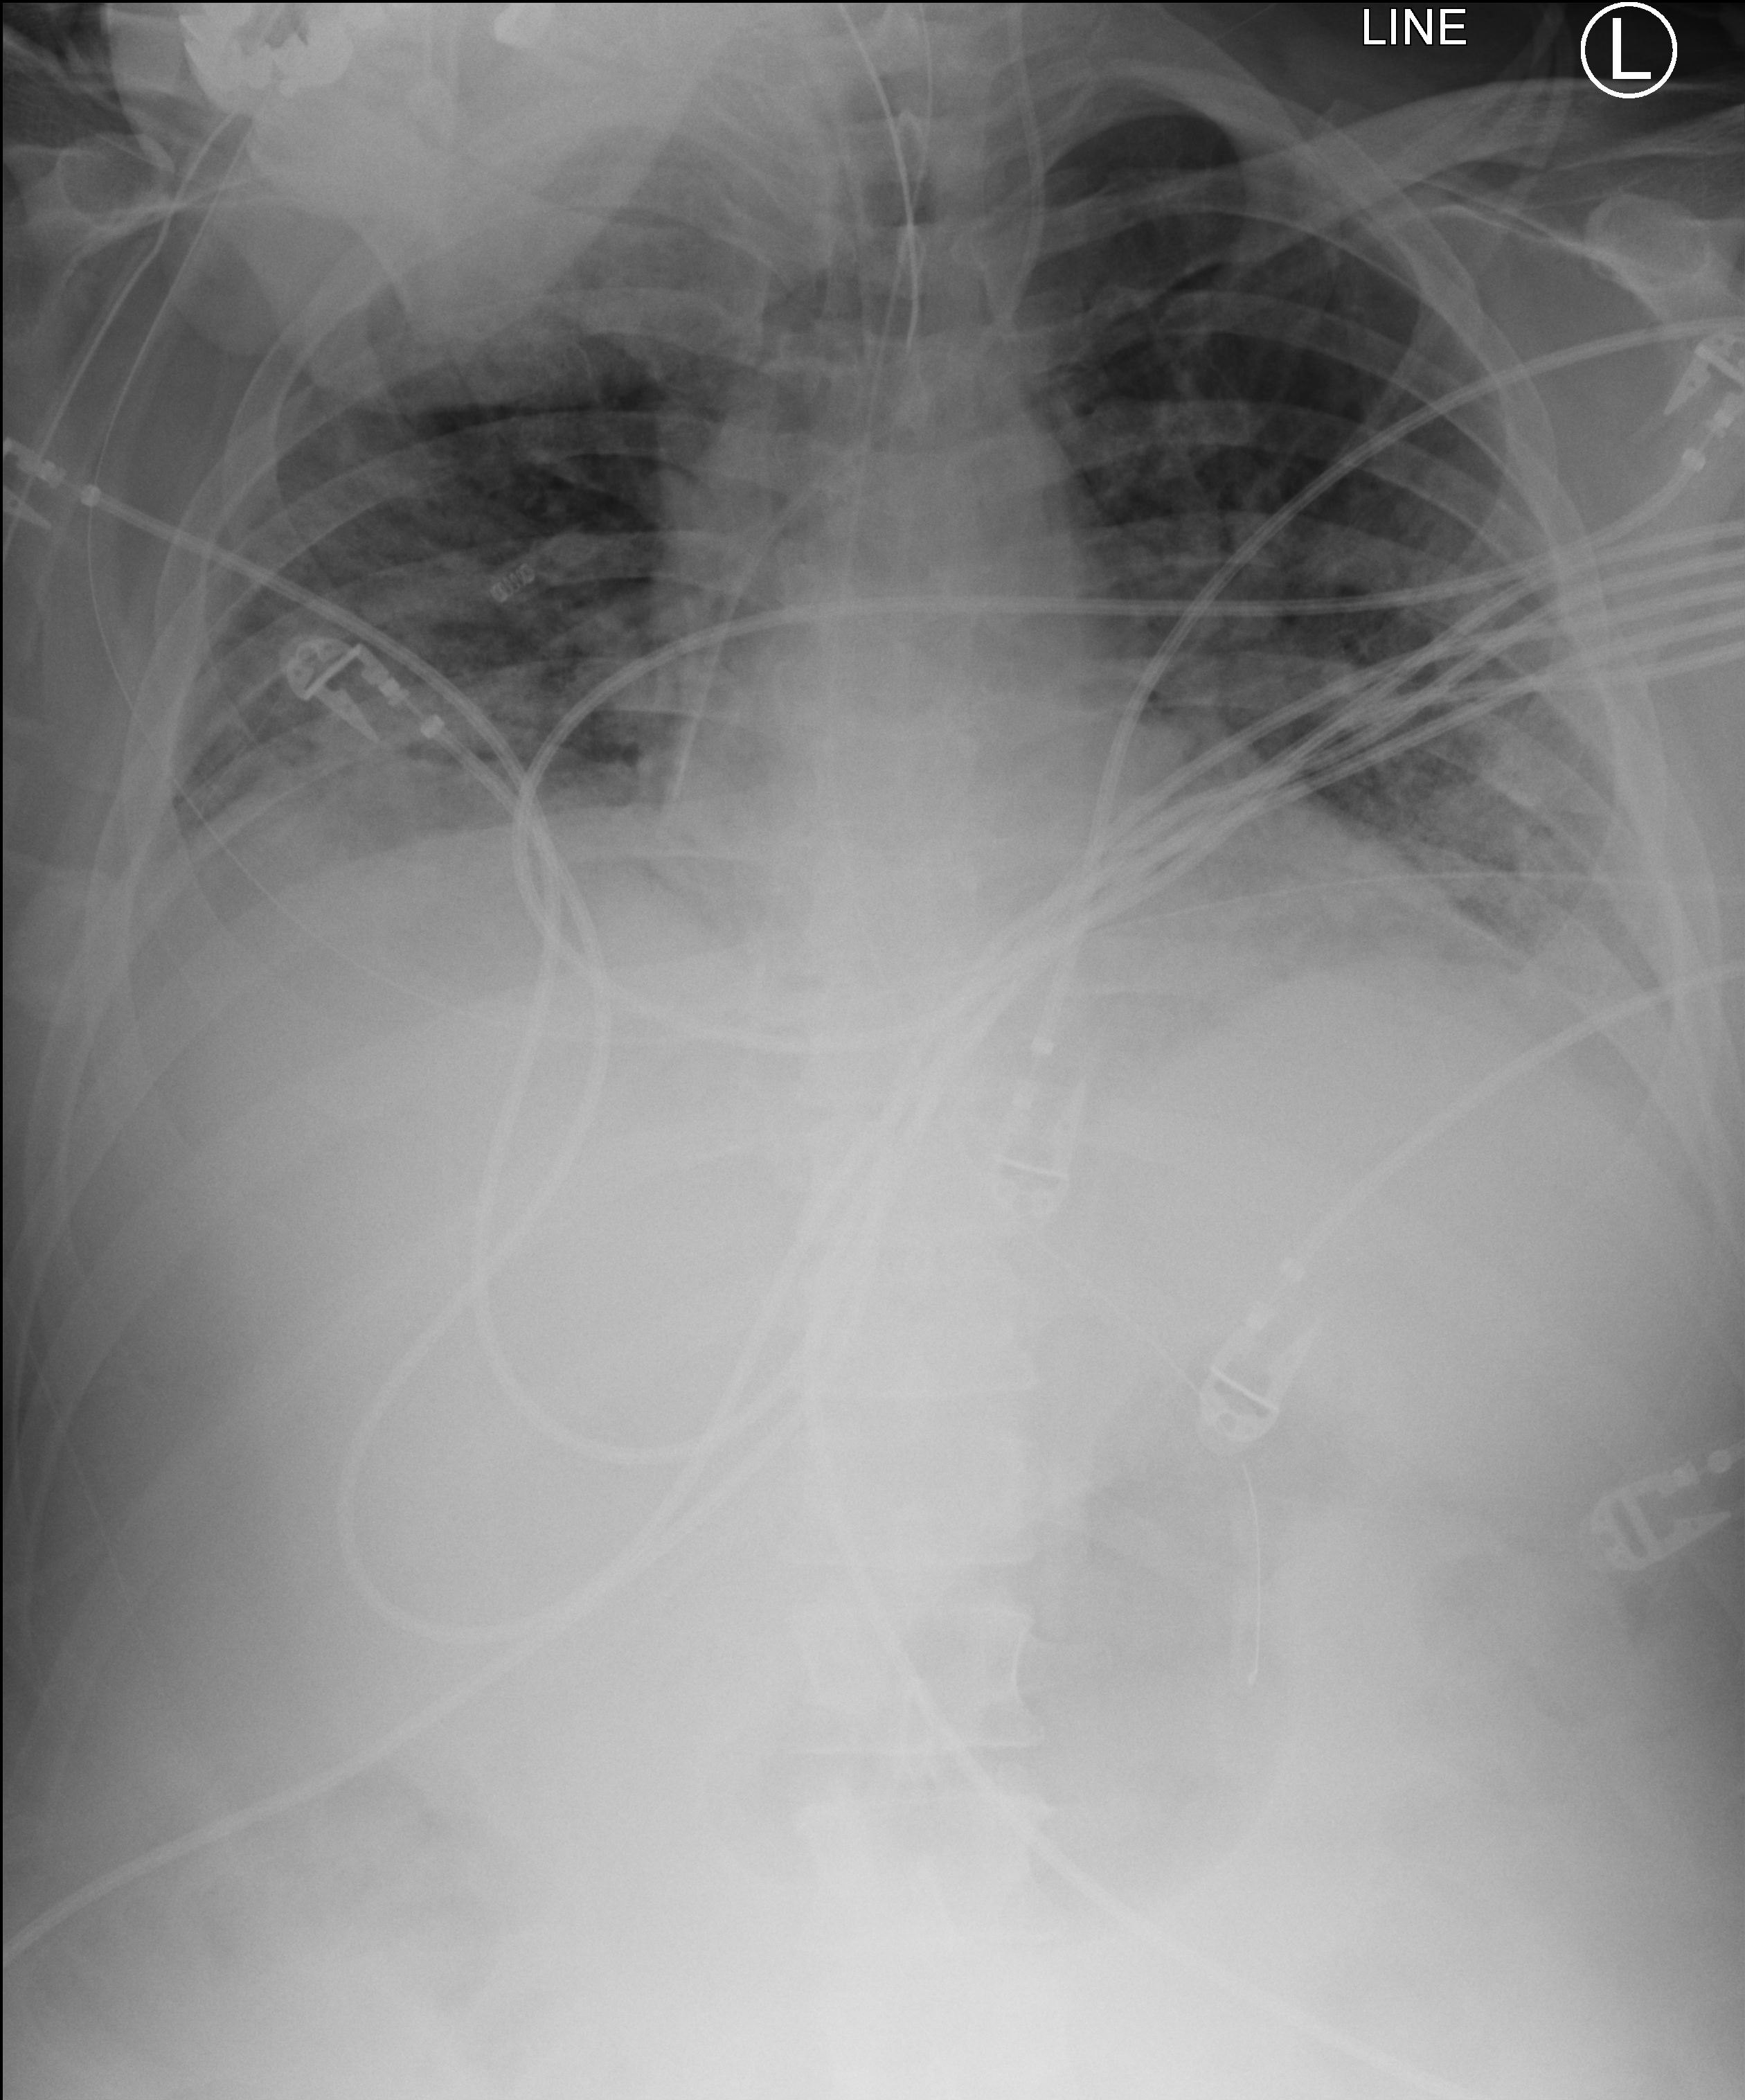
Chest X-ray (portable), anteroposterior (AP) projection. Patient hospitalised with COVID-19; male, aged 18–59 years.
From the hospital-stay record, not from the radiograph (when in the stay this image was taken is not recorded):
- admitted to intensive care during this hospital stay: yes
- chronic kidney disease (admission record): no